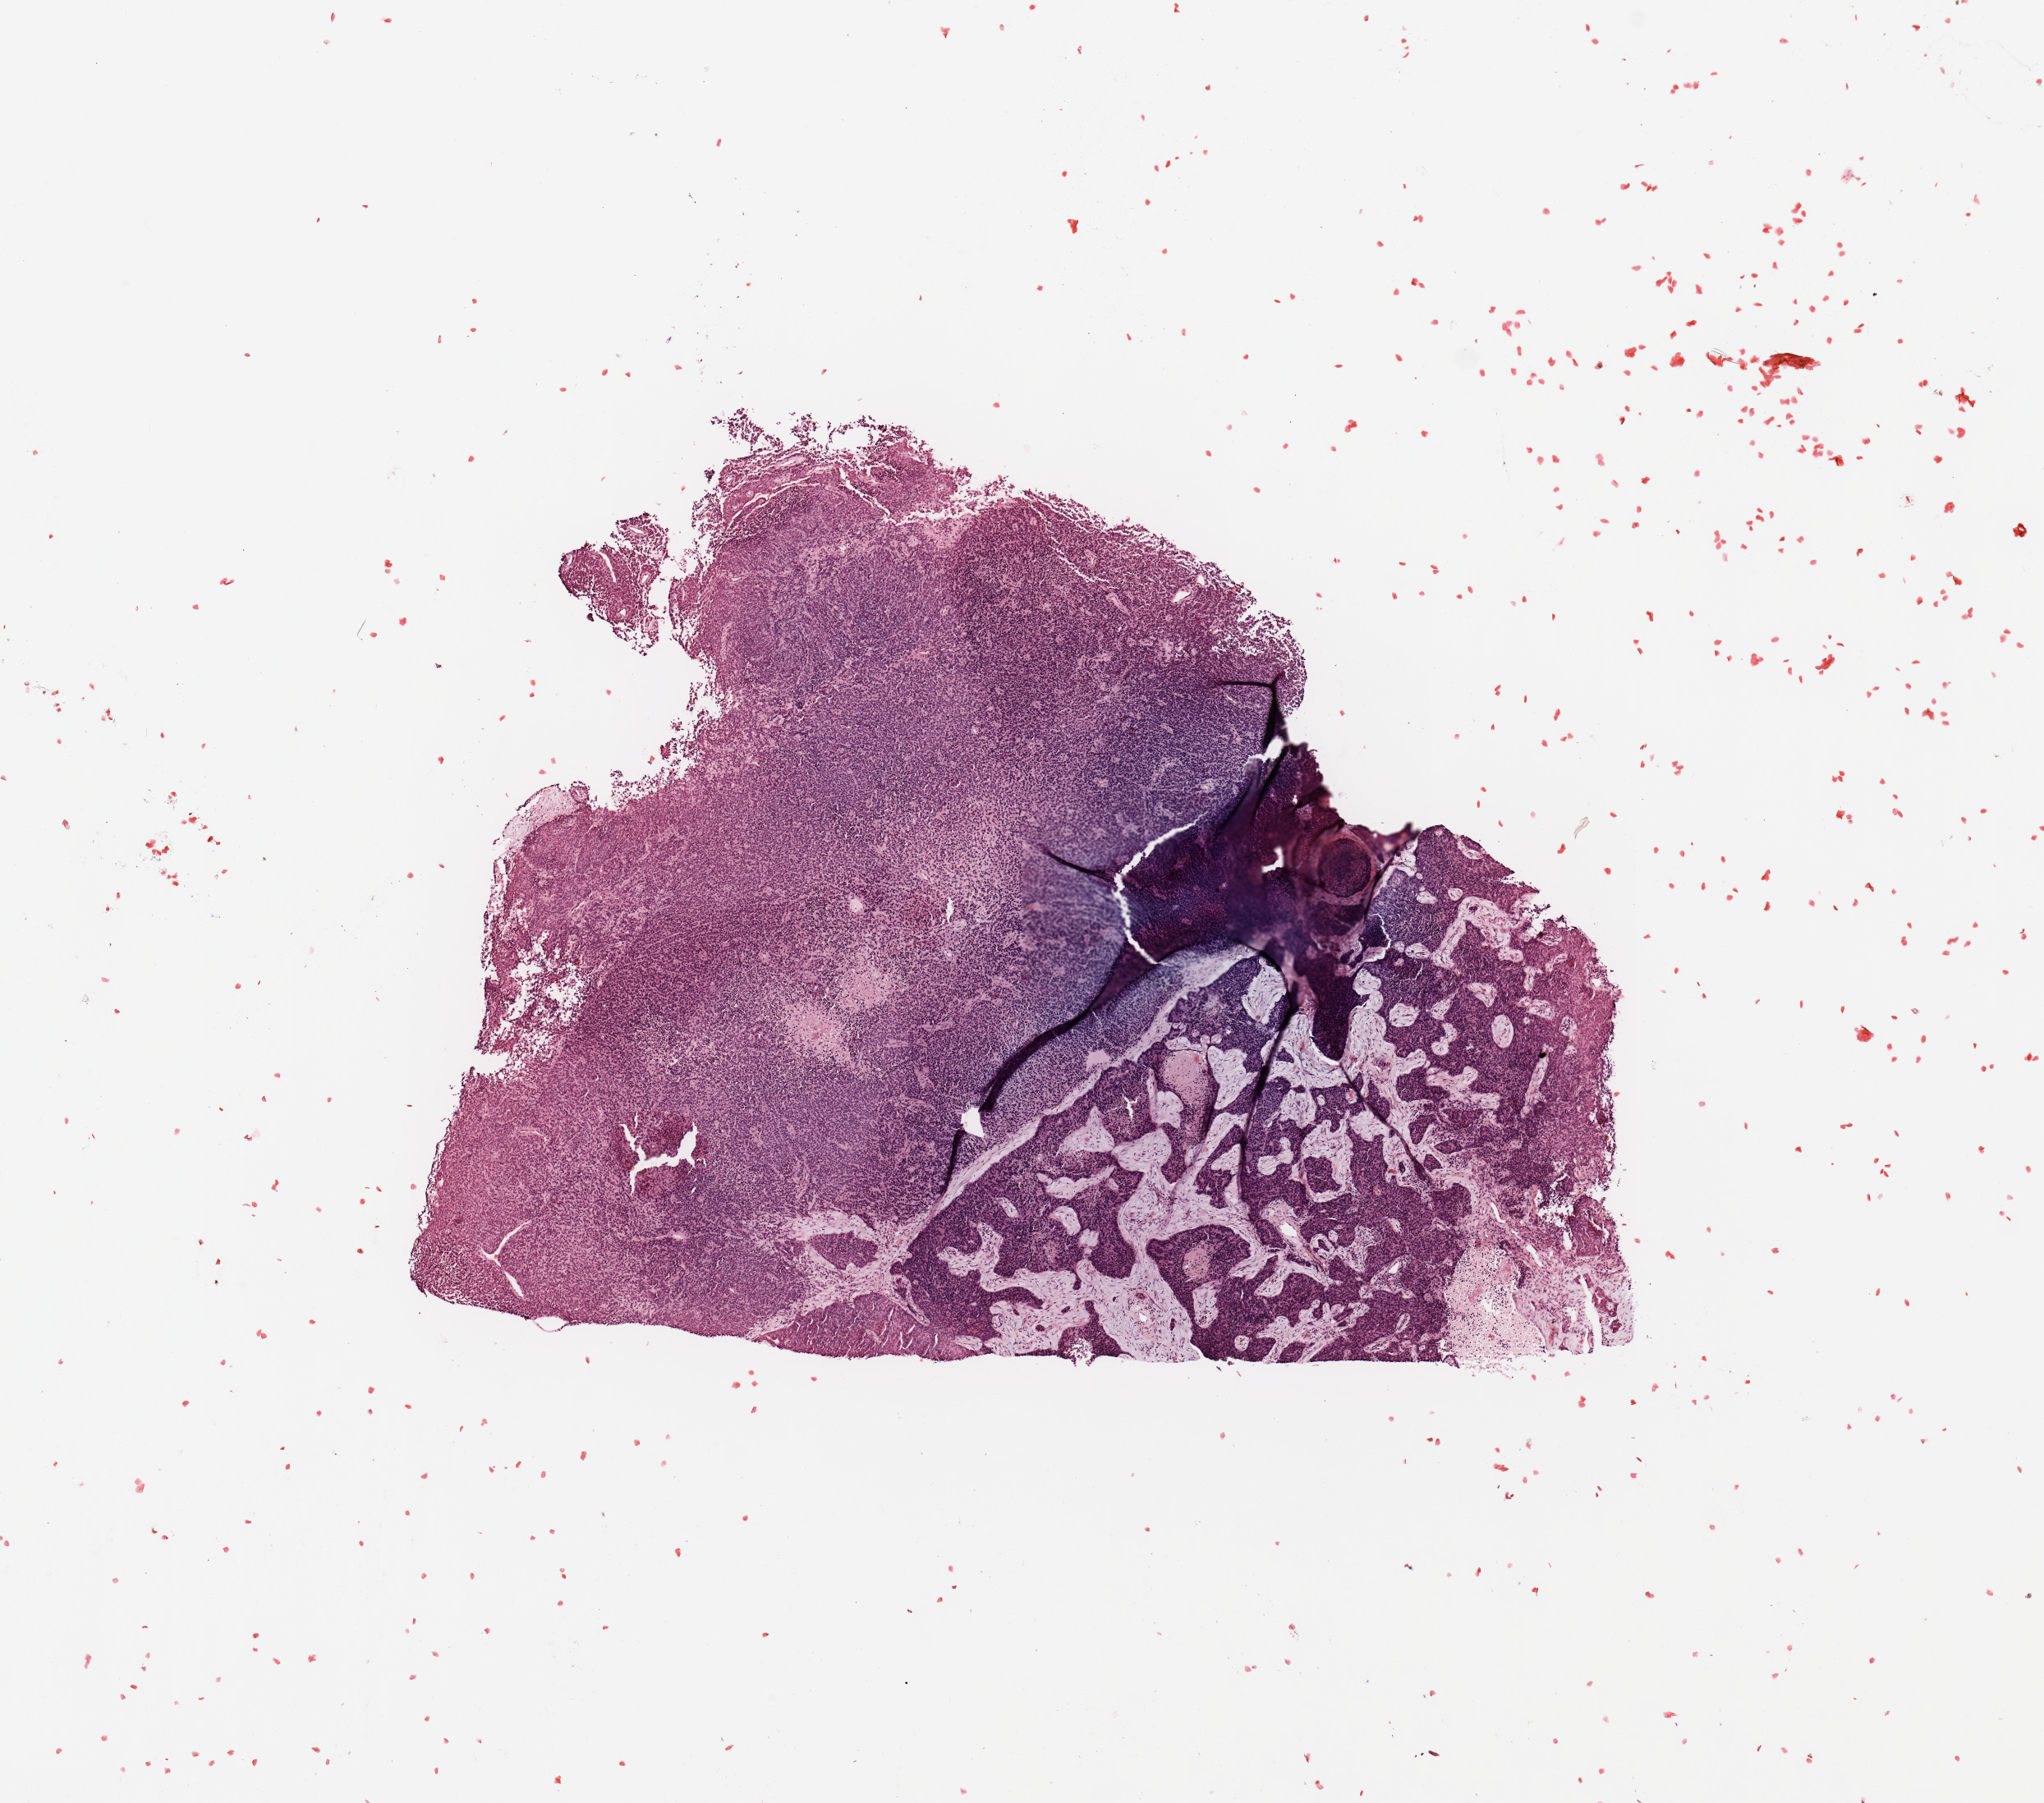
H&E-stained whole-slide image — low-resolution overview of the scanned area, about 9.8 x 8.7 mm (slide scanned at 20x); tumour tissue sample, lung. Patient: male, age 67 years. Histologic grade: GX (grade cannot be assessed).
Primary tumour site (as recorded): right upper lobe. Histologic diagnosis: Squamous cell carcinoma, NOS. AJCC pathologic stage: IIB.